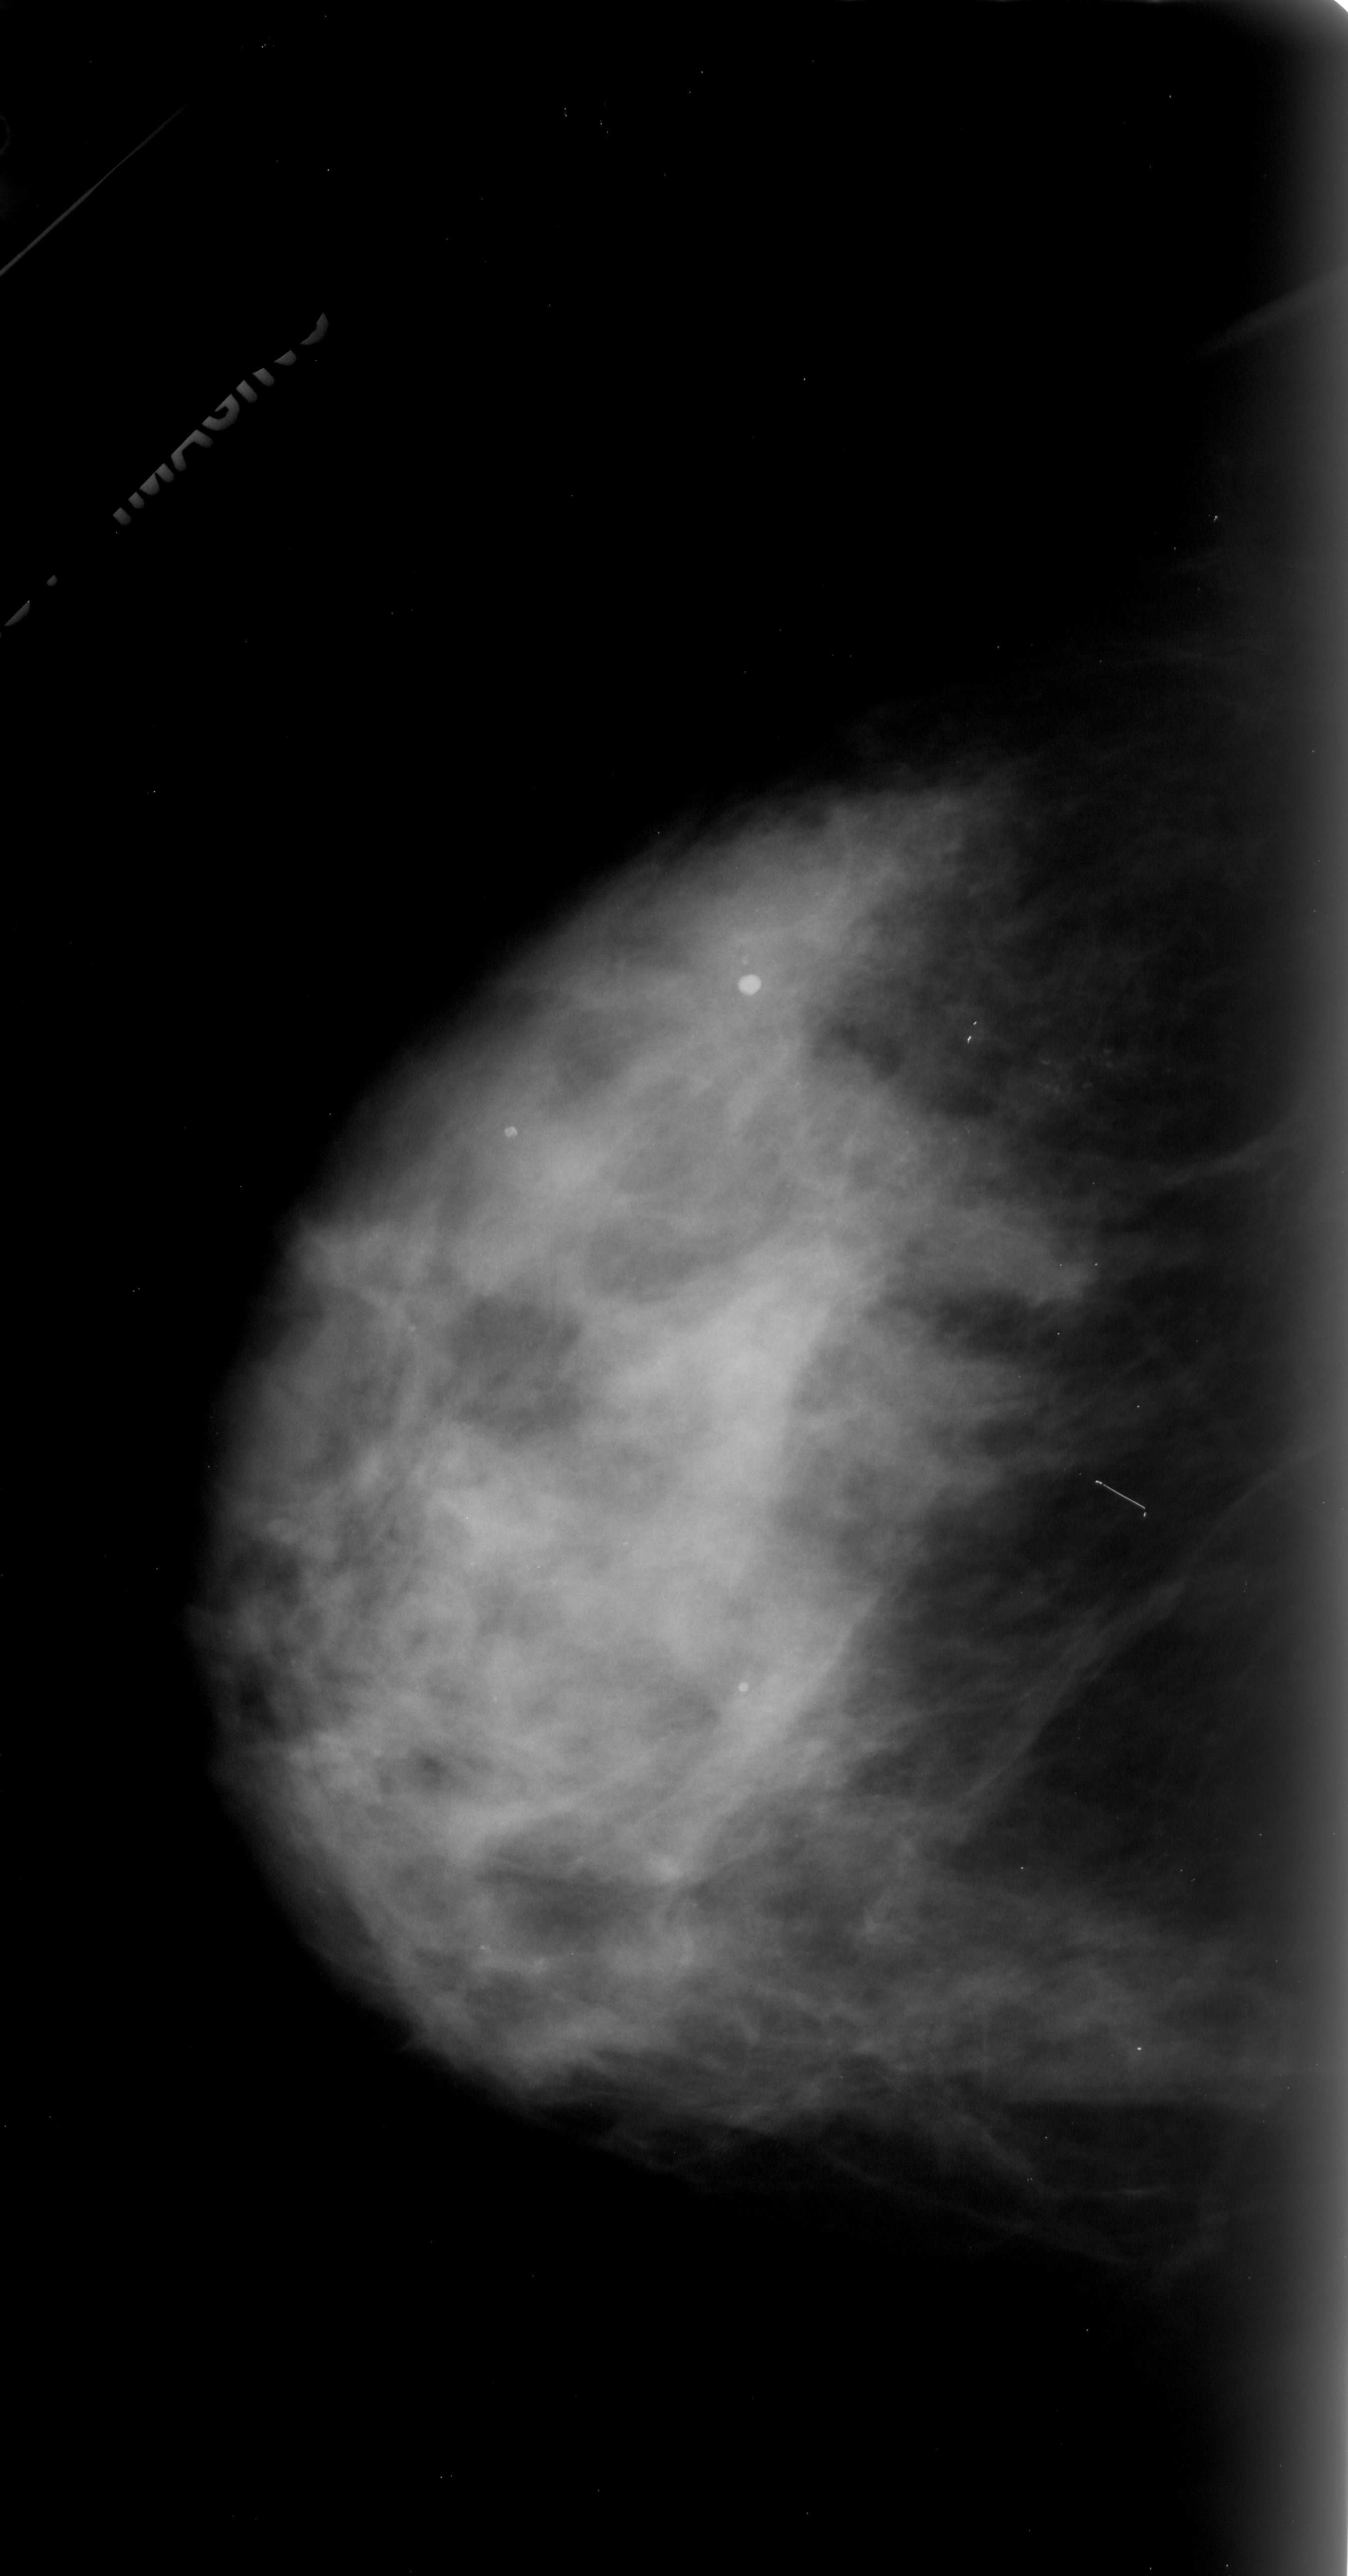
Scanned film-screen mammogram; left breast; craniocaudal (CC) view; BI-RADS breast density category 4 (scale 1–4); 1348 × 2576 image matrix.
Expert-marked regions of interest on this film, with their recorded descriptors:
- calcifications, morphology pleomorphic, distribution linear; BI-RADS assessment category 4; pathology (as recorded): malignant: bounding box [x1, y1, x2, y2] px = [856, 1019, 1155, 1197]